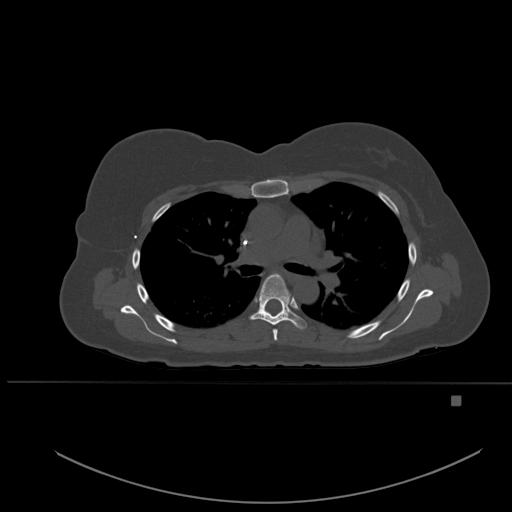
CT including the spine, one axial slice; position 367 of 651 along the scan axis; bone window (W 1800 / L 400 HU); 1.5 mm slice thickness; 512 × 512 image matrix, field of view 443 × 443 mm. Female patient, age 49 years. From the clinical record (not read from this slice): primary cancer: breast; vertebrae with lytic lesions (as recorded): L3, T12, L4.
Structures marked on this image (semi-automatic segmentation, software-assisted and operator-edited):
- T4 vertebra: box from (x=260, y=274) to (x=278, y=341) px
- T5 vertebra: (x=250, y=273)–(x=307, y=329)